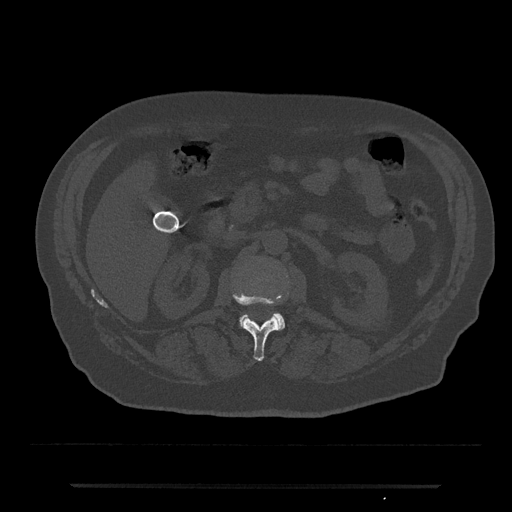
CT including the spine, one axial slice. Position 514 of 797 along the scan axis. 120 kVp. Bone window (W 1800 / L 400 HU). 512 × 512 image matrix, field of view 434 × 434 mm. Patient: male, 80 years. Case-level facts recorded for this patient, not image findings: primary cancer: prostate; vertebrae with lytic lesions (as recorded): L1, T11.
Annotated regions visible in this slice (semi-automatically segmented with operator editing):
- L1 vertebra: bounding box <234,294,283,361> (left, top, right, bottom; pixels)
- L2 vertebra: <239,312,285,331>